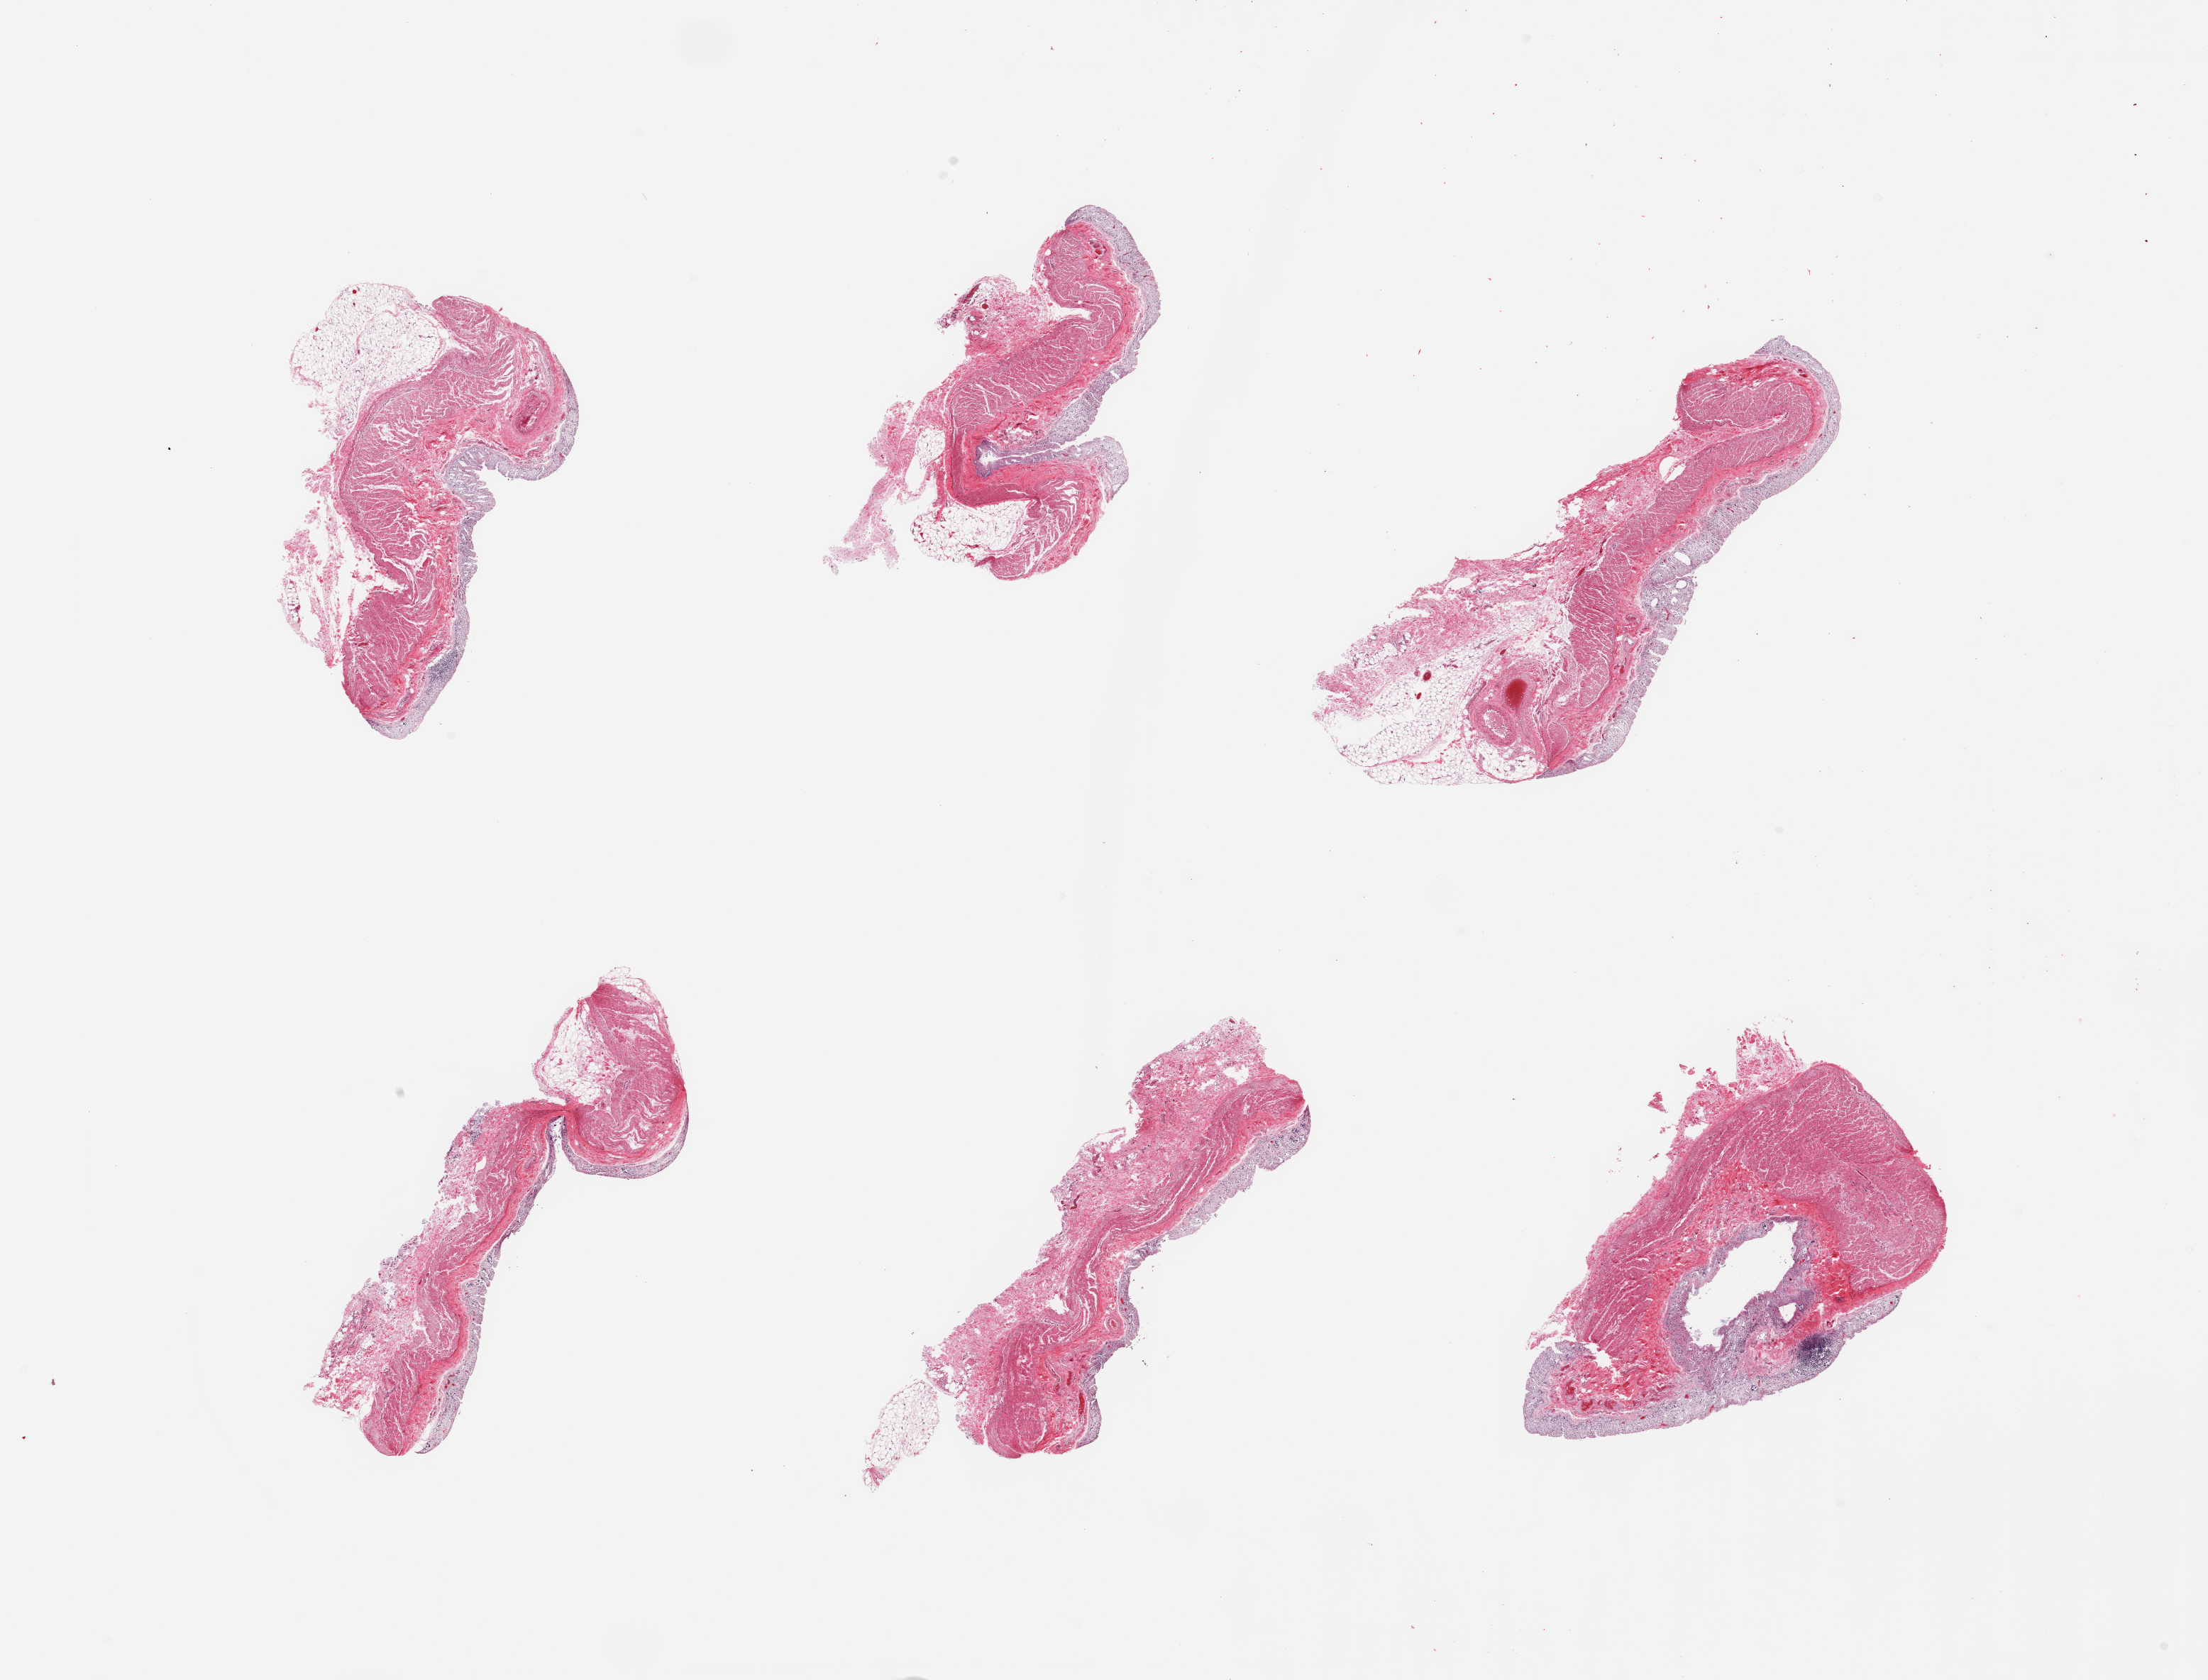
Hematoxylin and eosin (H&E) whole-slide image, shown as a low-resolution overview of the whole scanned area (about 24.6 x 18.7 mm, slide scanned at 20x), PAXgene-fixed, paraffin-embedded tissue, target tissue: transverse colon, donor tissue sample. Donor: male.
Reviewer comment on this tissue sample: 6 pieces, mucosa is ~0.5mm, glandular elements completely sloughed, advanced autolysis.